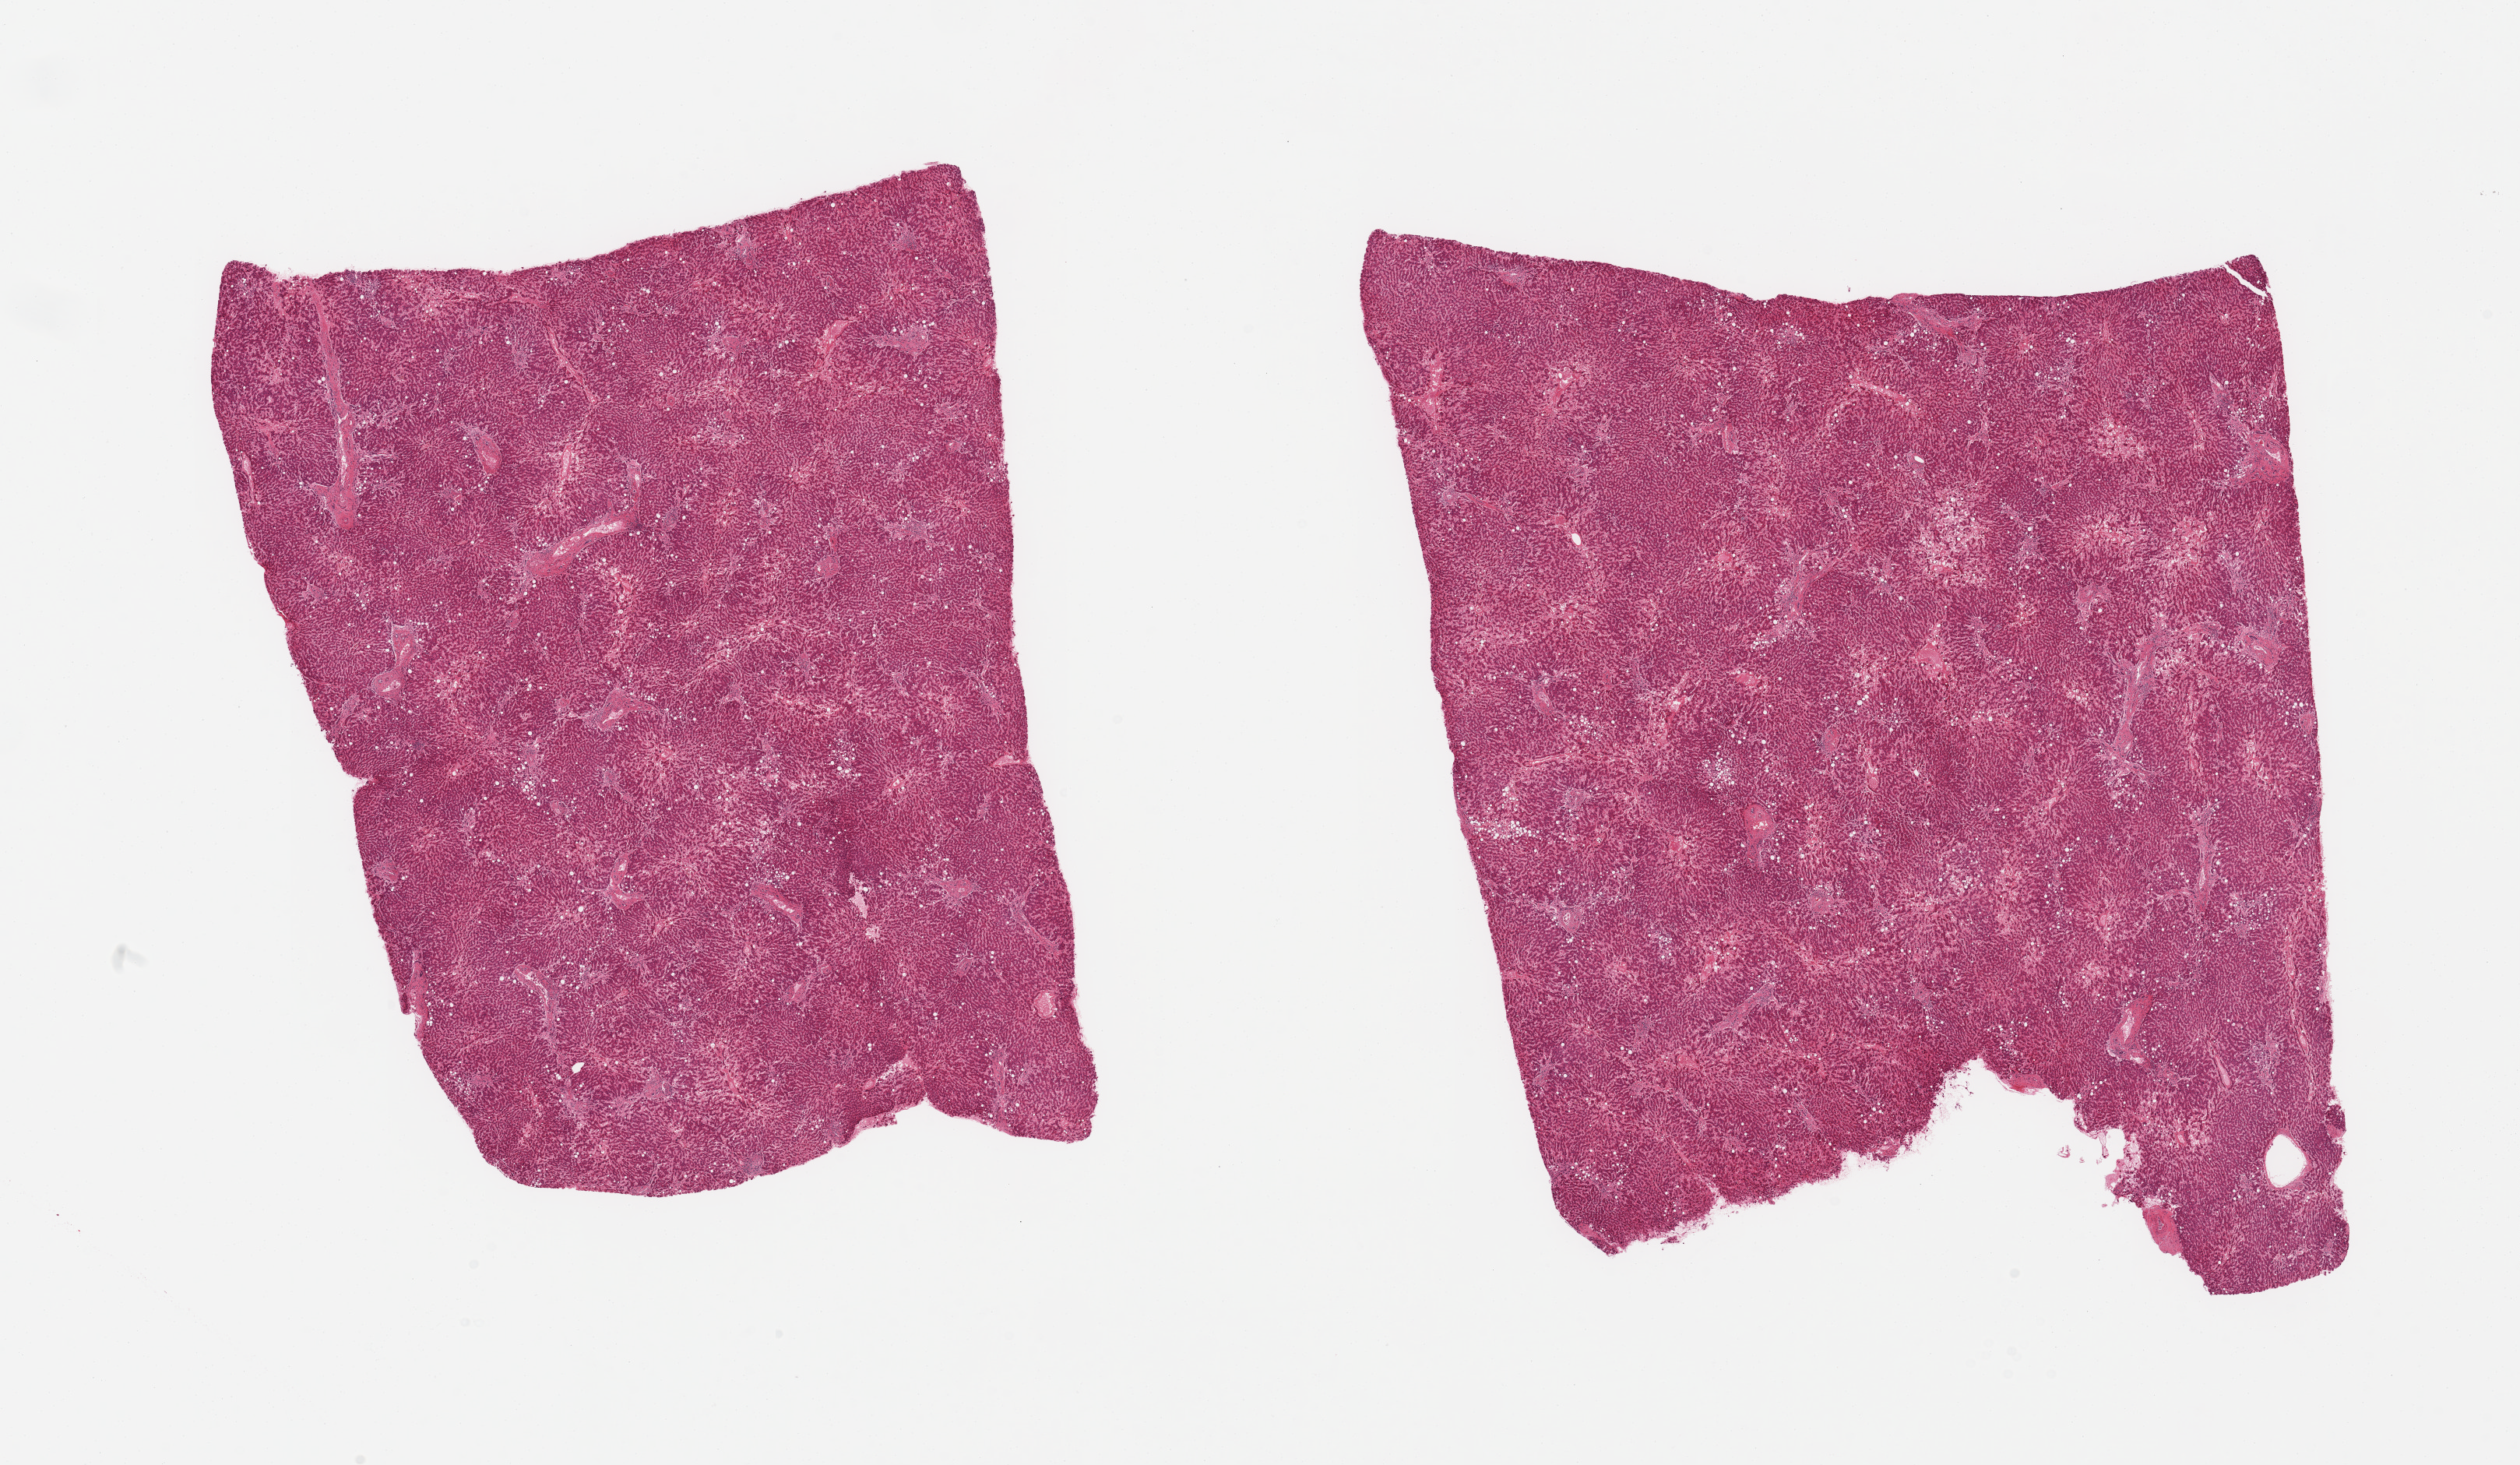
Hematoxylin and eosin (H&E) whole-slide image, shown as a low-resolution overview of the whole scanned area (about 25.6 x 14.9 mm); PAXgene-fixed paraffin-embedded (PFPE) section; sampled site (target tissue): liver; tissue donor sample.
* pathologist's review note for this sample: 2 pieces, mild chronic steatohepatitis, mild early bridging fibrosis, moderate passive congestion